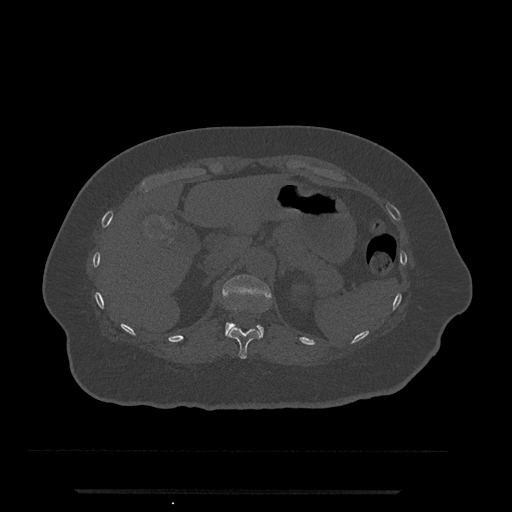
CT including the spine, one axial slice; position 203 of 797 along the scan axis; bone window (W 1800 / L 400 HU); 512 × 512 image matrix. Patient: female, 51 years. Case-level facts recorded for this patient, not image findings: primary cancer: neuro.
Structures marked on this image (semi-automatic segmentation, software-assisted and operator-edited):
- T11 vertebra: bounding box [x1, y1, x2, y2] px = [226, 327, 261, 359]
- T12 vertebra: [222, 274, 271, 337]